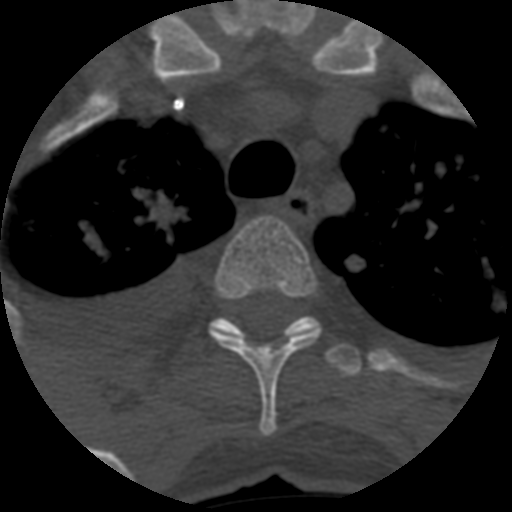
CT including the spine, one axial slice; slice 483 of 708 in the series (ordered by position); one of 3 acquisitions stored at this slice position; bone window (W 1800 / L 400 HU); 1.25 mm slice thickness; 512 × 512 image matrix, field of view 160 × 160 mm. Patient age 55 years. Case-level facts recorded for this patient, not image findings: primary cancer: colon.
Structures marked on this image (semi-automatically segmented with operator editing):
- T3 vertebra: box from (x=209, y=217) to (x=319, y=436) px
- T4 vertebra: (x=211, y=316)–(x=362, y=377)